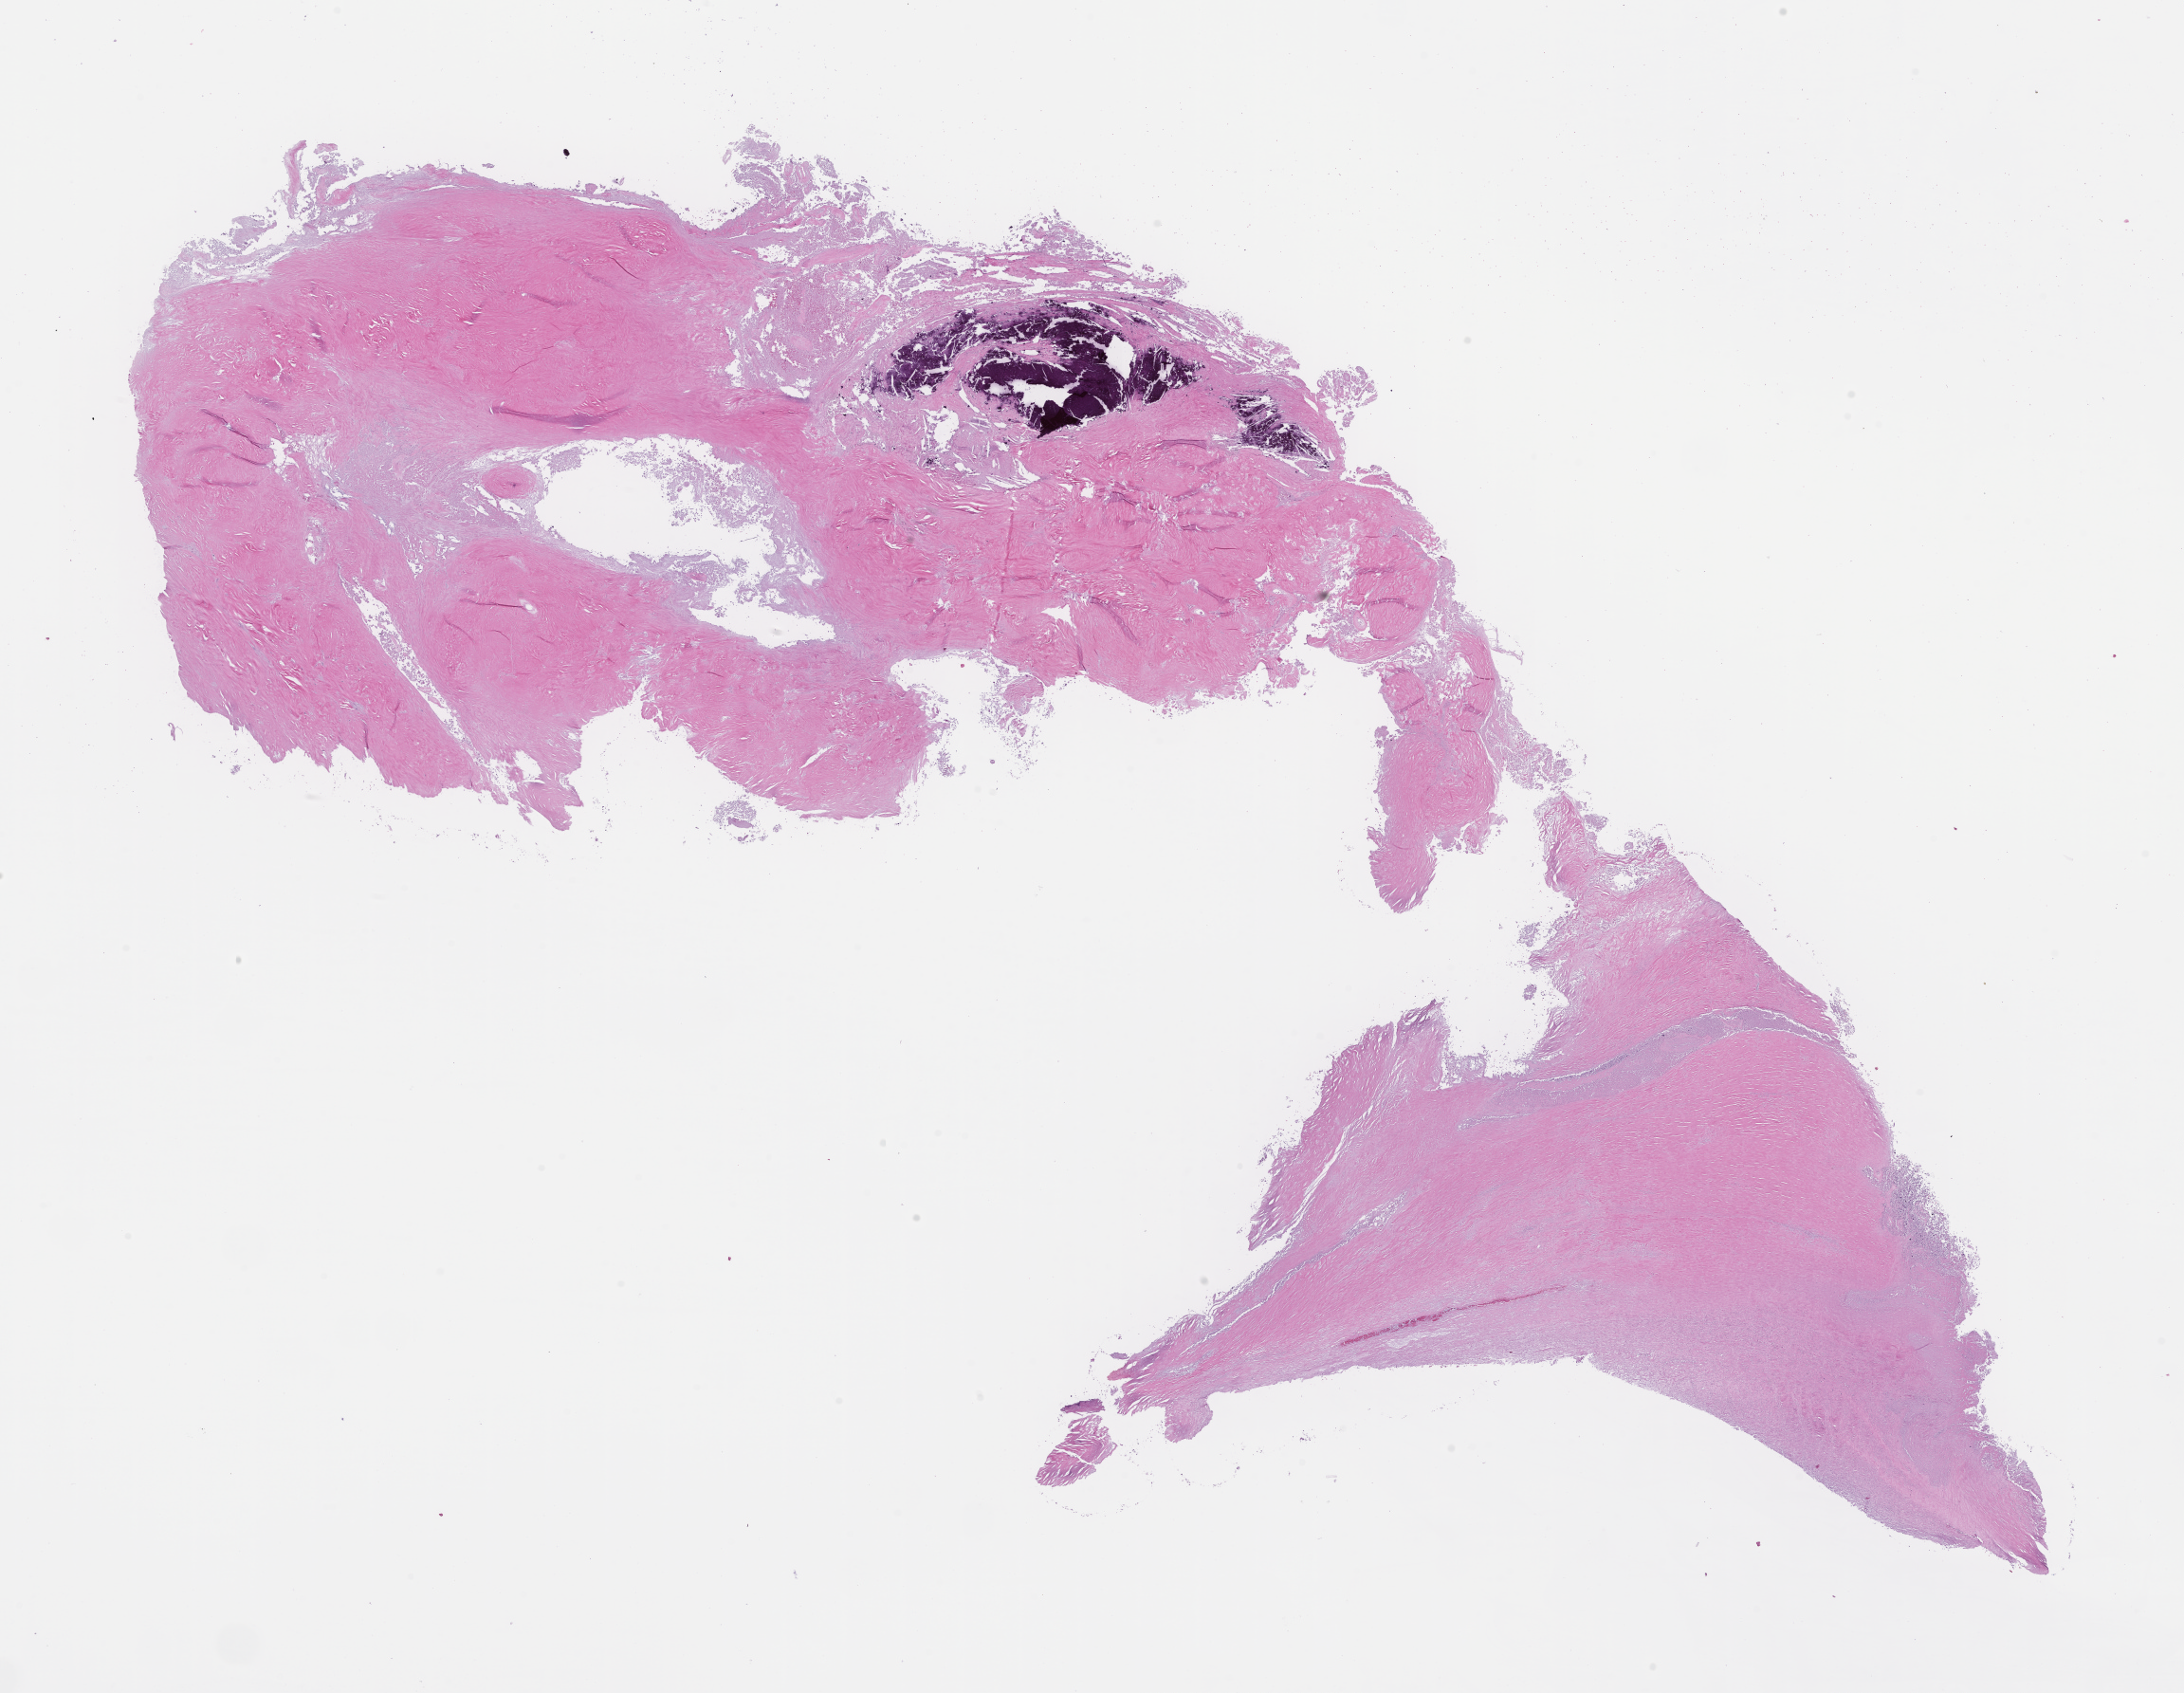
Digitized haematoxylin and eosin-stained section, whole scanned area (about 18.6 x 14.4 mm) shown as a low-resolution overview. Formalin-fixed, paraffin-embedded (FFPE) tissue. Tissue site: ovary. Patient: female.
• this section: primary tumor
• diagnosis: Ovarian Carcinoma